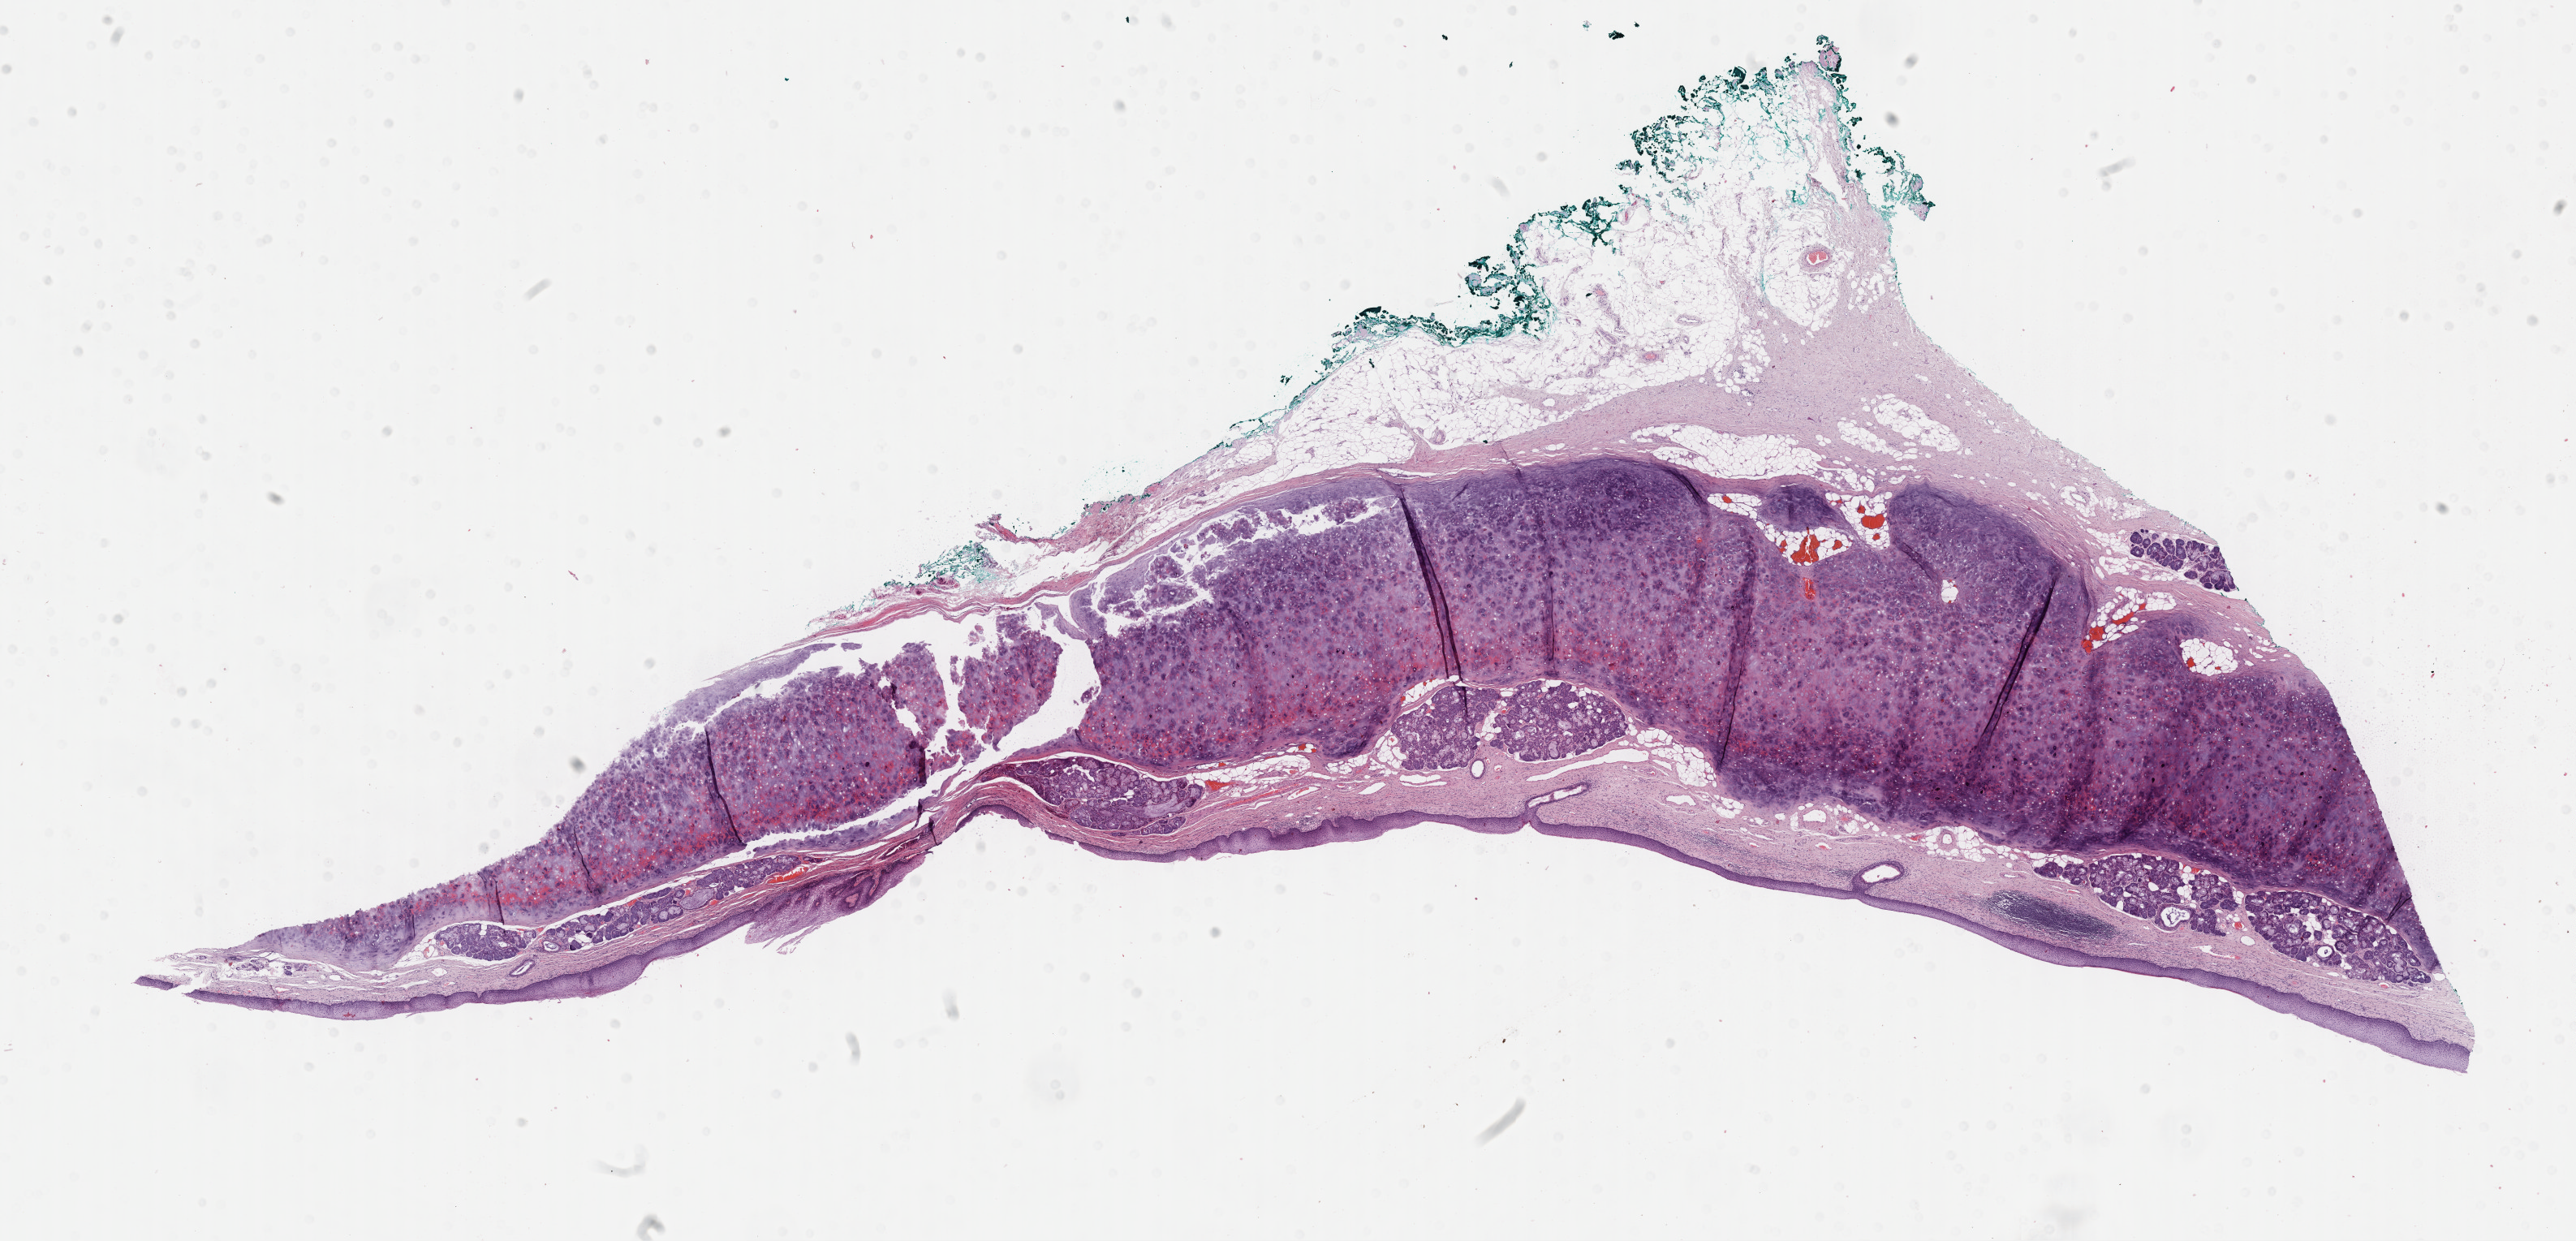
Digitized H&E tissue section (whole slide) — whole scanned area (about 25.7 x 12.4 mm) shown as a low-resolution overview; formalin-fixed paraffin-embedded (FFPE) diagnostic section; sample: primary tumour, head and neck. Male patient; age at initial diagnosis 67 years. Histologic grade: G1 (well differentiated).
Diagnosis: Squamous cell carcinoma, keratinizing, NOS (larynx, NOS). Lymph nodes positive (case pathology): 1 of 3 examined. Laterality: right. AJCC pathologic stage: III (7th edition).